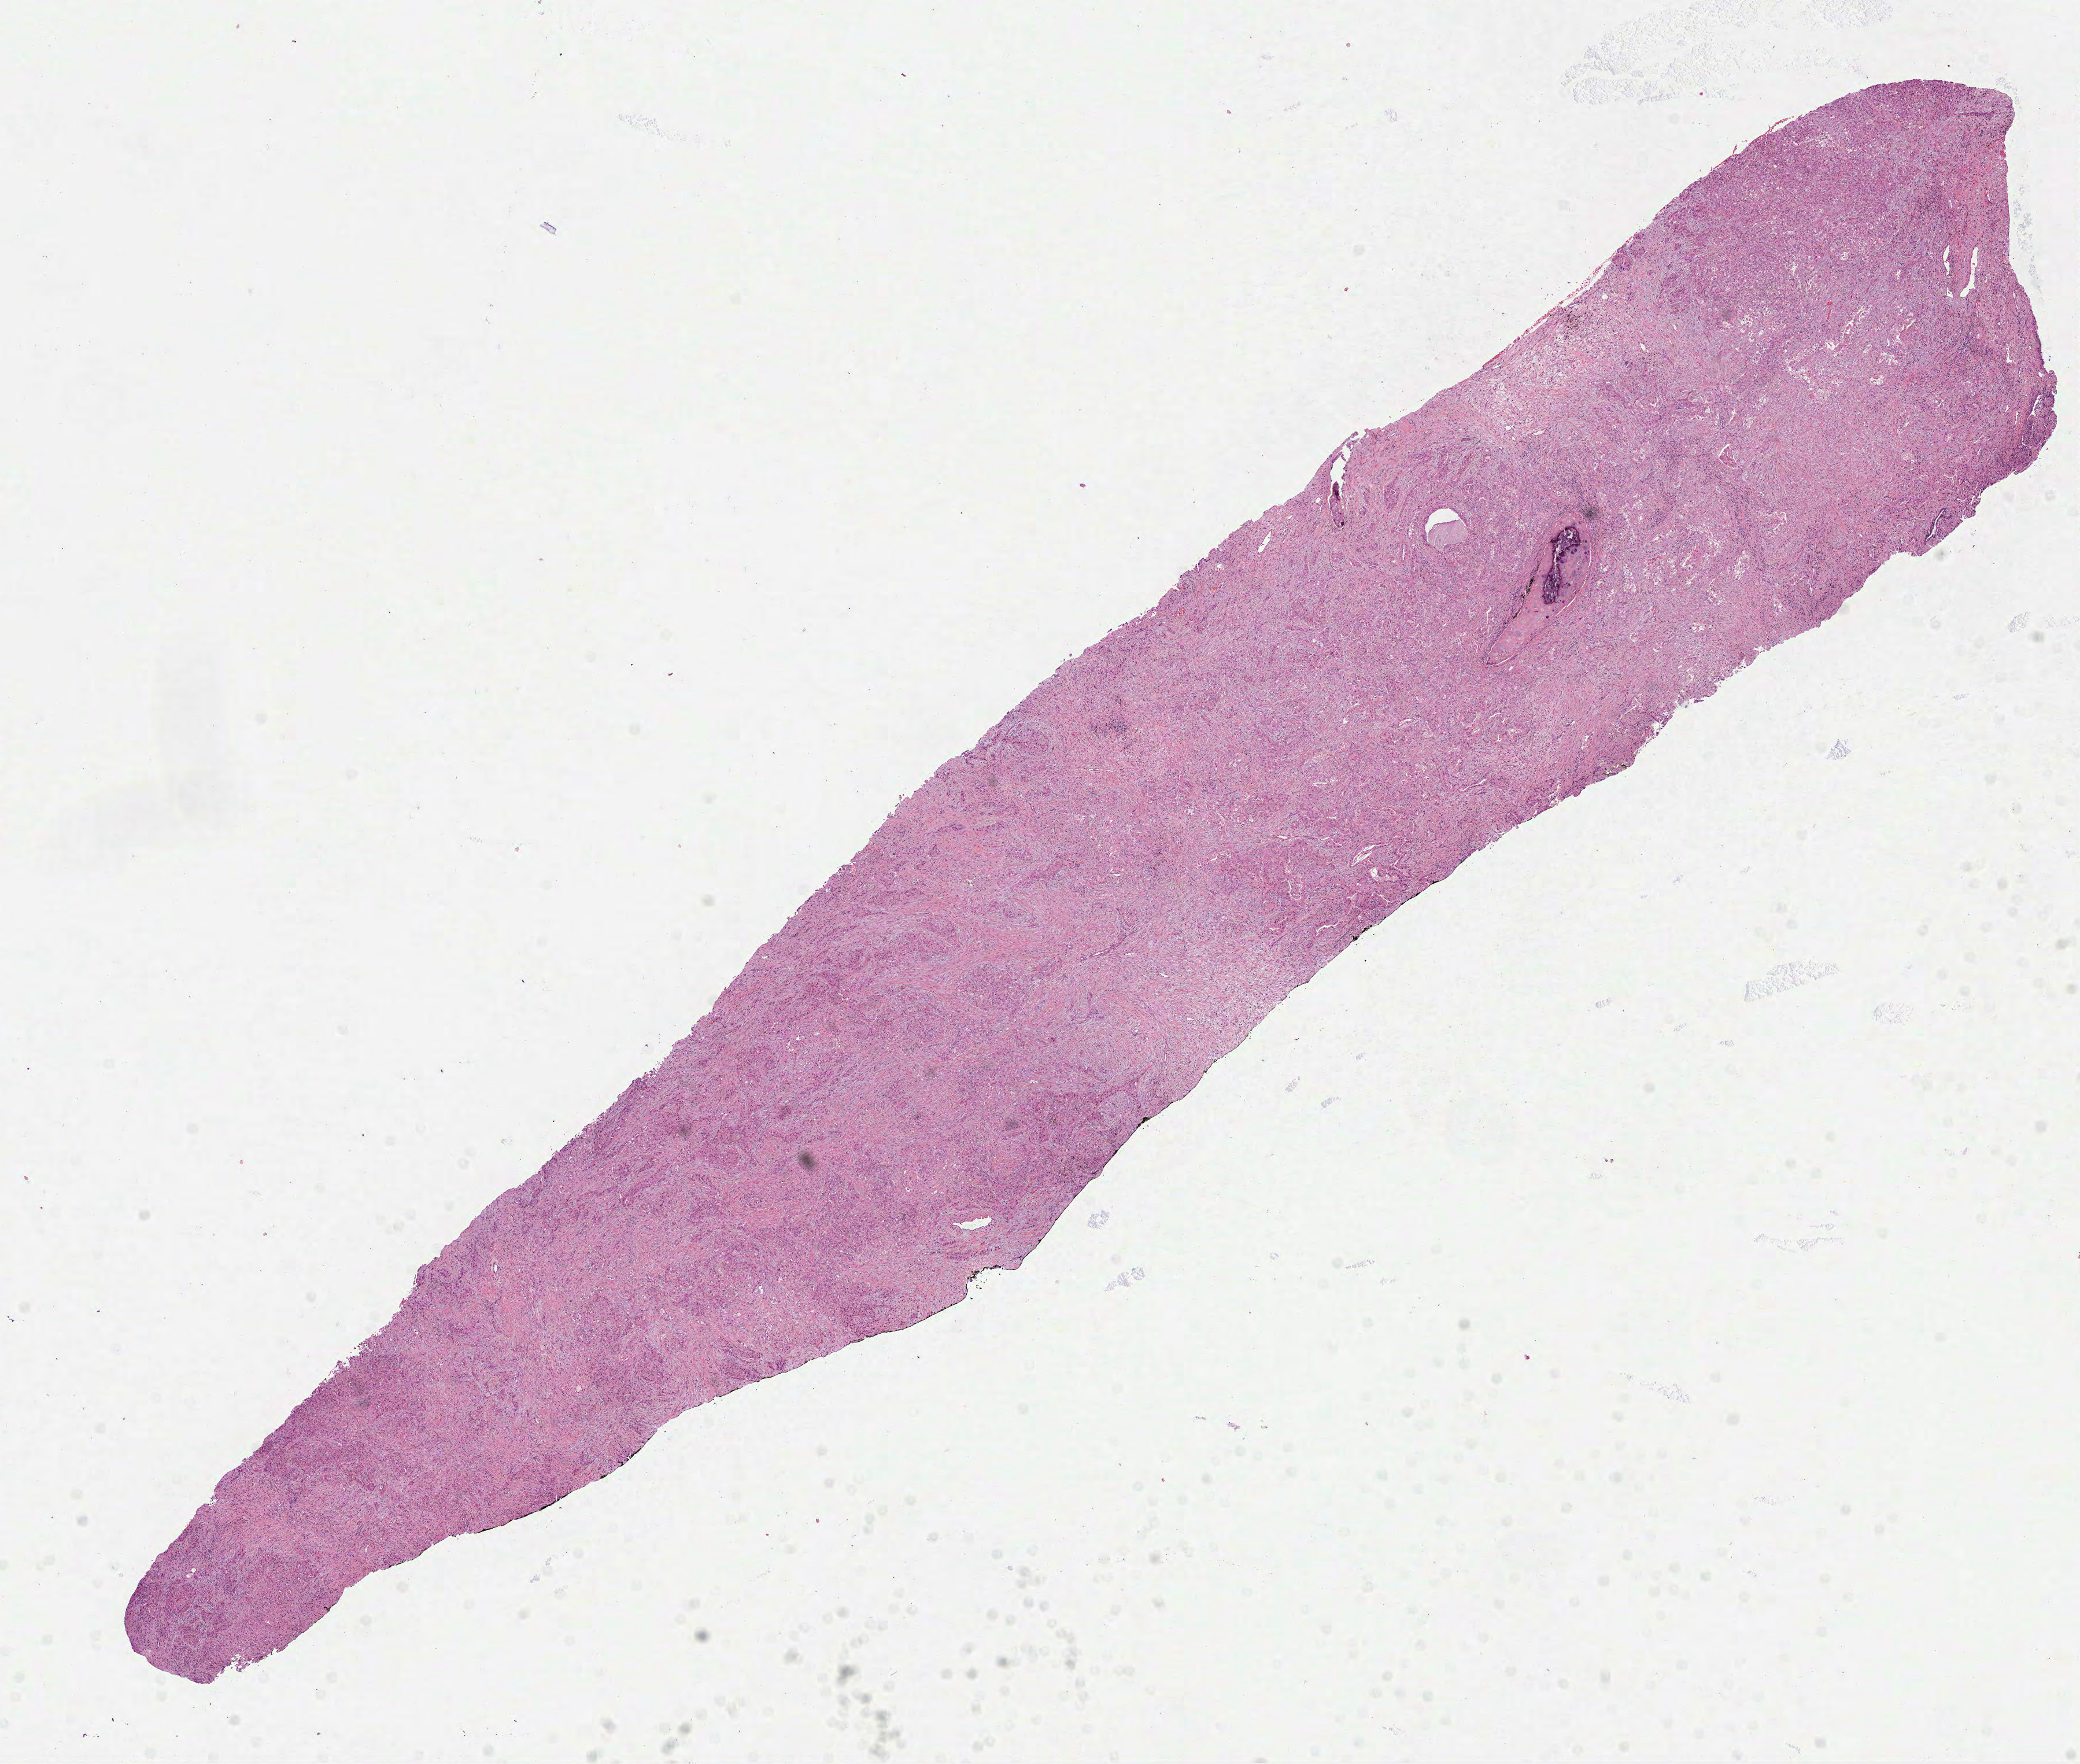
H&E whole-slide image, shown as a low-resolution overview of the whole scanned area (about 14.5 x 12.3 mm); formalin-fixed paraffin-embedded (FFPE) diagnostic section; sample: primary tumour, lung. Female, age 79 years at initial diagnosis.
• laterality: right
• AJCC pathologic stage: IIB
• histologic diagnosis: Adenocarcinoma, NOS (lower lobe, lung)